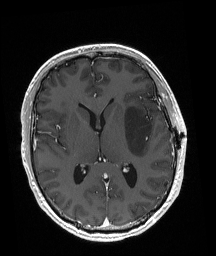
Brain MRI from a brain-tumour surgery series, one axial slice. Slice 96 of 192 in the series (ordered by position). T1-weighted post-contrast. 216 × 256 image matrix, field of view 211 × 250 mm. From the clinical record (not read from this slice): histopathology: Astrocytoma; WHO grade: 3; IDH mutation: yes; tumour location: Left Posterior Frontal.
Annotated regions visible in this slice (outlined manually by an expert reader):
- tumour: bounding box [x1, y1, x2, y2] px = [124, 107, 152, 157]